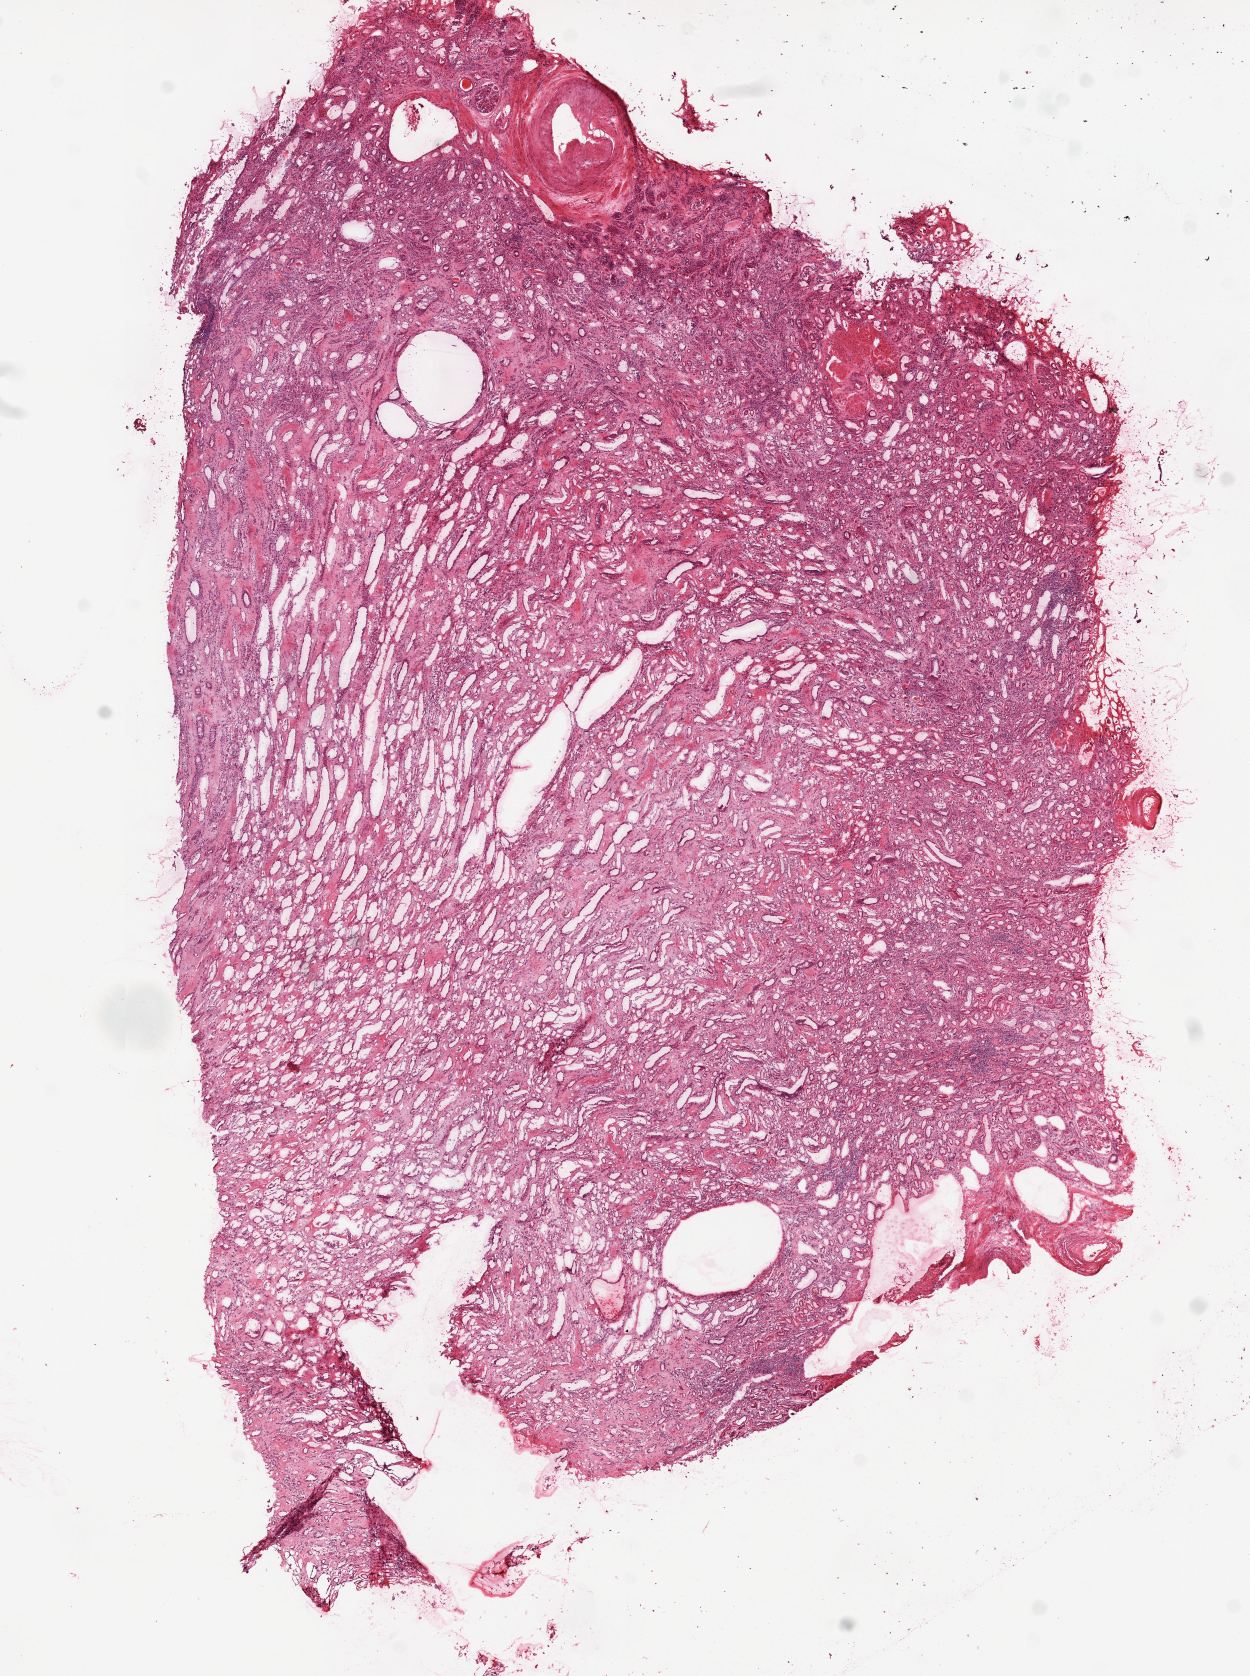
H&E-stained whole-slide image, a low-resolution overview of the entire scanned area, about 10.0 x 13.4 mm (slide scanned at 20x), frozen section from the top of the tissue portion, solid tissue normal (non-tumour tissue) sample from the kidney. Male patient; age at initial diagnosis 88 years.
This section: solid tissue normal sample (biorepository sample class). Patient diagnosis: Clear cell adenocarcinoma, NOS.